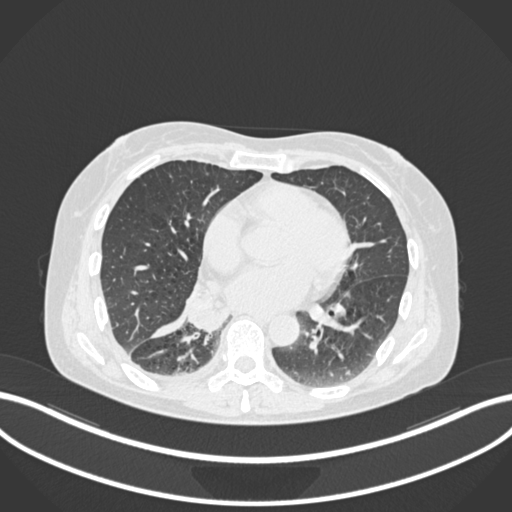
Chest CT, one axial slice; position 68 of 168 along the scan axis; reconstruction kernel B30f; lung window (W 1500 / L -600 HU); 512 × 512 image matrix, field of view 400 × 400 mm. Patient: female, 63 years. Case-level facts recorded for this patient, not image findings: clinical TNM (as recorded): T1c N0 M0.
Annotated regions visible in this slice (bounding box drawn by a radiologist):
- lung tumour (recorded histology: adenocarcinoma): bounding box [x1, y1, x2, y2] px = [180, 282, 233, 335]